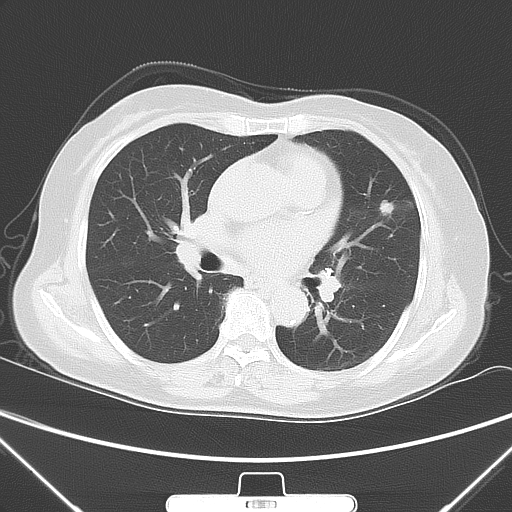
Chest CT, one axial slice. Slice 30 of 60 in the series (ordered by position). Lung window (W 1500 / L -600 HU). 5 mm slice thickness. 512 × 512 image matrix, field of view 350 × 350 mm. Patient: female, 70 years. From the clinical record (not read from this slice): clinical TNM (as recorded): T1b N0 M0.
Structures marked on this image (bounding box drawn by a radiologist):
- lung tumour (recorded histology: adenocarcinoma): bounding box [x1, y1, x2, y2] px = [377, 194, 395, 218]